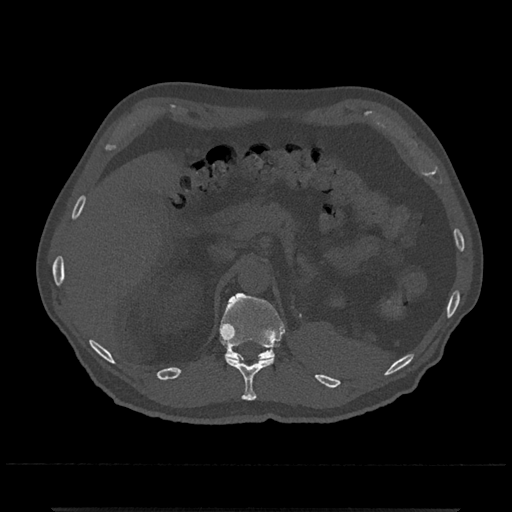
CT including the spine, one axial slice. Position 460 of 797 along the scan axis. 120 kVp. Bone window (W 1800 / L 400 HU). 0.5 mm slice thickness. 512 × 512 image matrix, field of view 393 × 393 mm. Patient: male, 67 years. Case-level facts recorded for this patient, not image findings: primary cancer: prostate.
Structures marked on this image (semi-automatic segmentation, software-assisted and operator-edited):
- T11 vertebra: box from (x=225, y=356) to (x=275, y=401) px
- T12 vertebra: (x=219, y=293)–(x=286, y=361)